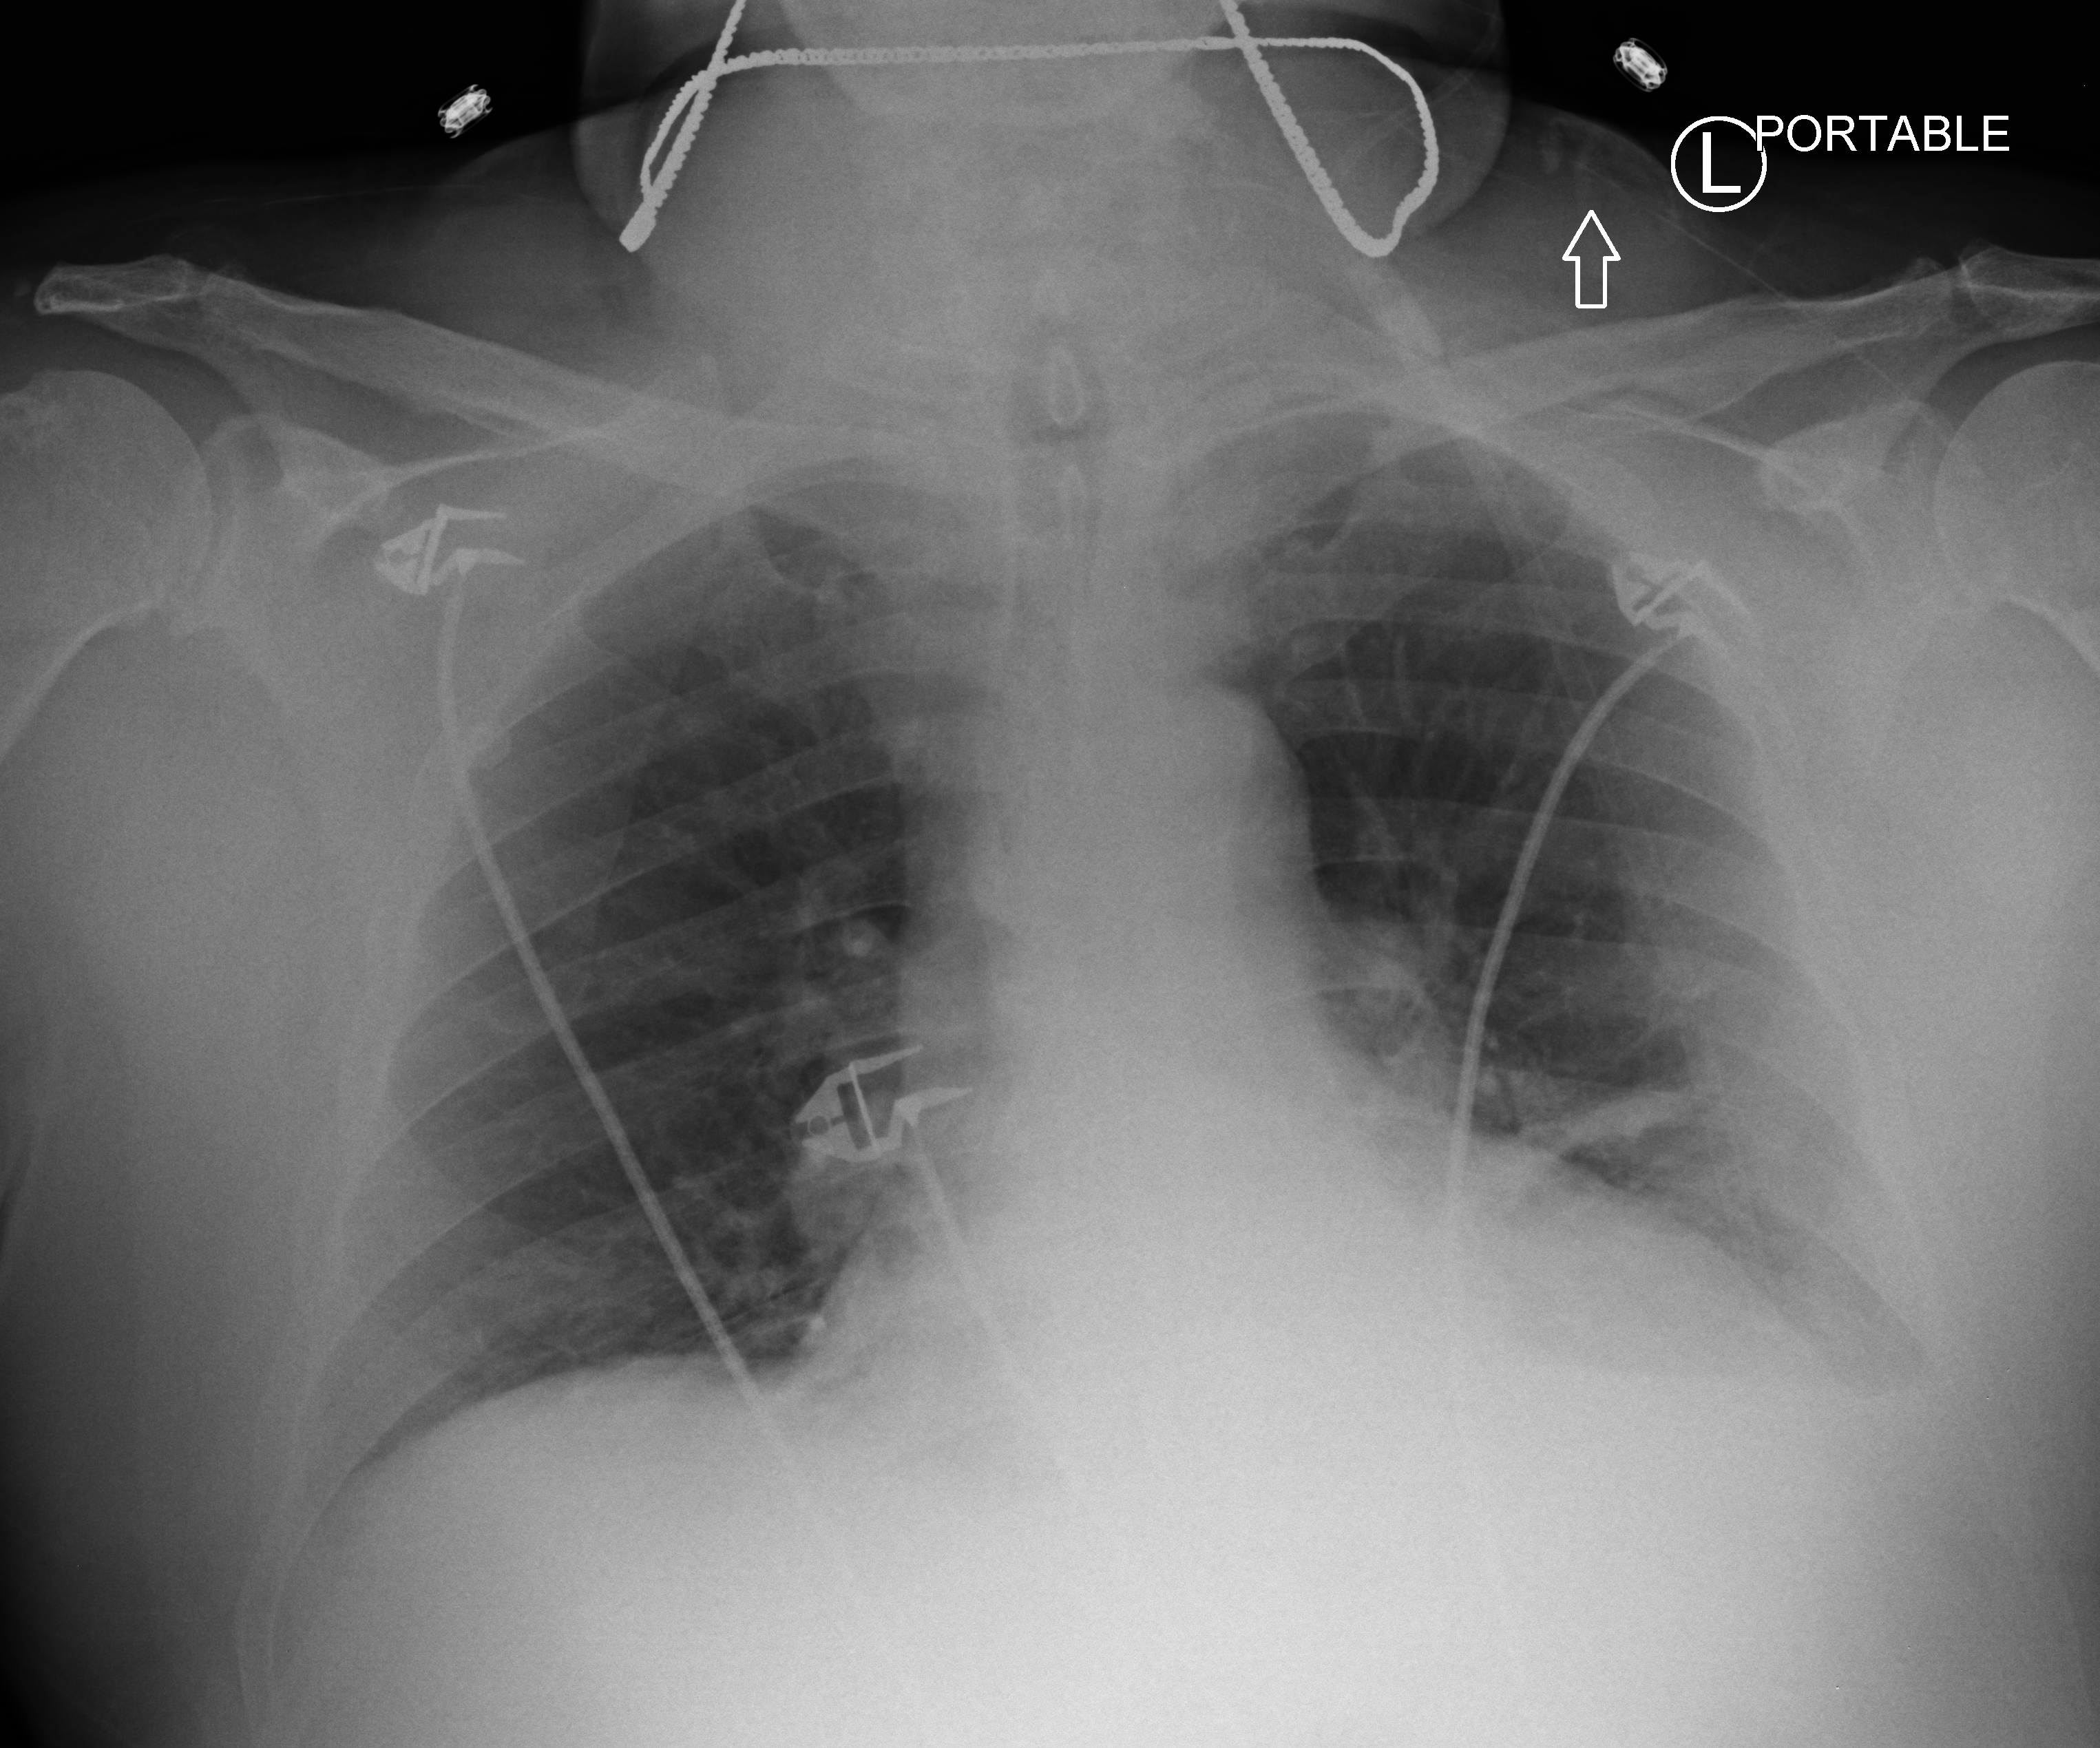
Chest X-ray (portable), anteroposterior (AP) projection. Patient hospitalised with COVID-19; male, aged 60–74 years.
Admission-level facts for this patient (not findings on this image; timing relative to this image not recorded):
- other chronic lung disease (admission record): yes
- length of hospital stay: 7 days